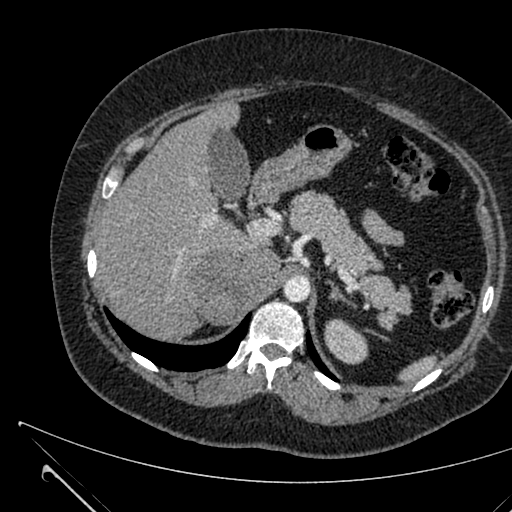
Contrast-enhanced abdominal CT, one axial slice. Position 453 of 731 along the scan axis. 120 kVp. Intravenous contrast given. Soft-tissue window (W 400 / L 40 HU). 1 mm slice thickness. 512 × 512 image matrix. Patient: female, 36 years. Case-level facts recorded for this patient, not image findings: diagnosis: adrenocortical carcinoma; tumour side: right adrenal; tumour size at pathology: 10 cm; Ki-67 index: 20 %; stage (as recorded): 4.
Structures marked on this image (semi-automatically segmented with operator editing):
- mass: bounding box <186,249,278,322> (left, top, right, bottom; pixels)